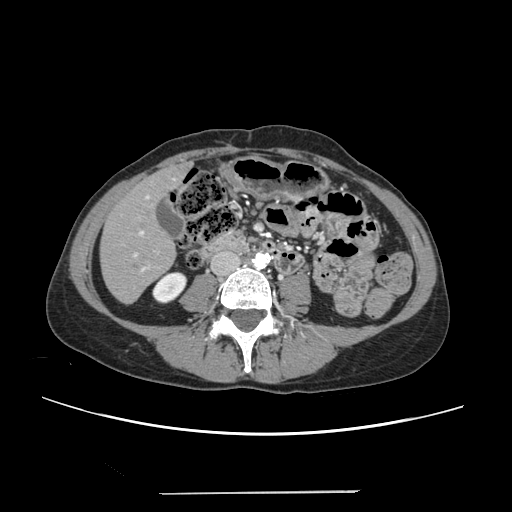
Contrast-enhanced abdominal CT, one axial slice; slice 65 of 240 in the series (ordered by position); 120 kVp; intravenous contrast given; soft-tissue window (W 400 / L 40 HU); 1.25 mm slice thickness; 512 × 512 image matrix. Female patient, age 60 years. From the clinical record (not read from this slice): diagnosis: colorectal cancer liver metastases, imaged before liver resection; multiple liver metastases: no; largest metastasis: 1.5 cm; disease in both lobes: no.
Structures marked on this image (outlined manually by an expert reader):
- liver: bounding box [x1, y1, x2, y2] px = [102, 167, 186, 302]
- planned liver remnant (the part of the liver to remain after resection): [102, 171, 176, 302]
- portal vein (with intrahepatic branches): [133, 196, 158, 271]